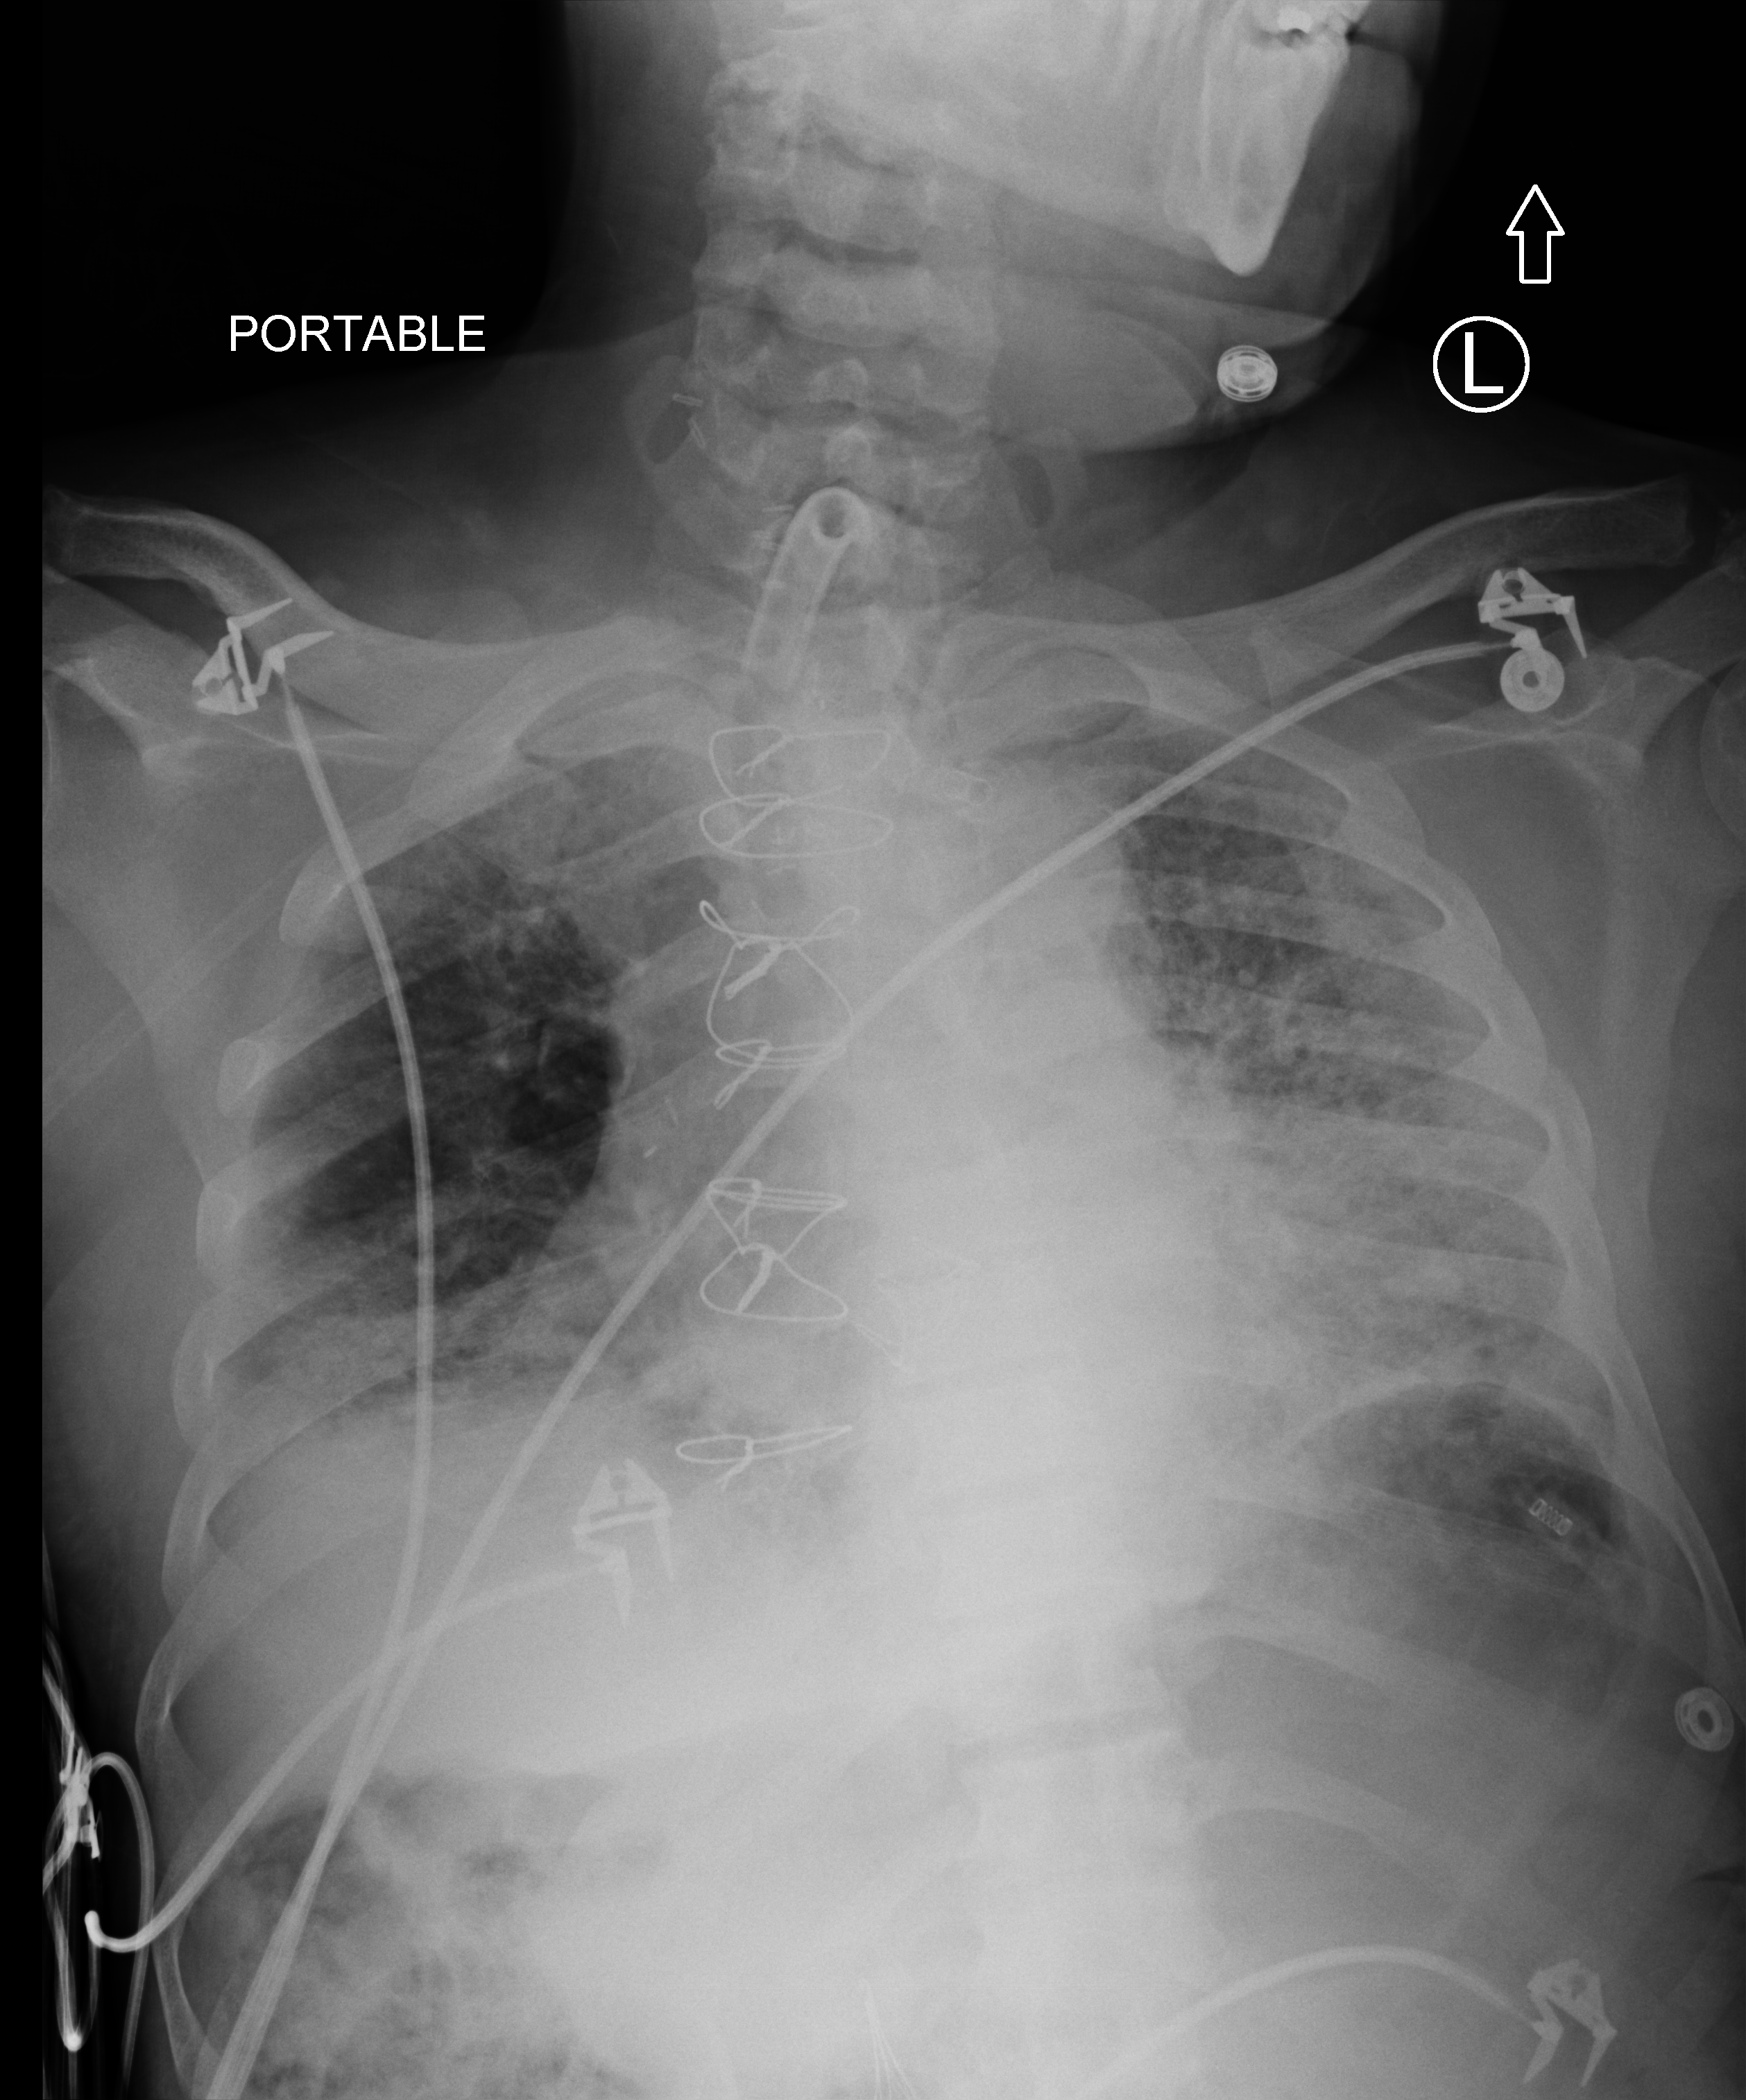
Portable chest radiograph. Male patient hospitalised with COVID-19, age 60–74 years.
Admission-level facts for this patient (not findings on this image; timing relative to this image not recorded):
- smoking status (admission record): never
- mechanically ventilated during this hospital stay: yes
- admitted to intensive care during this hospital stay: yes